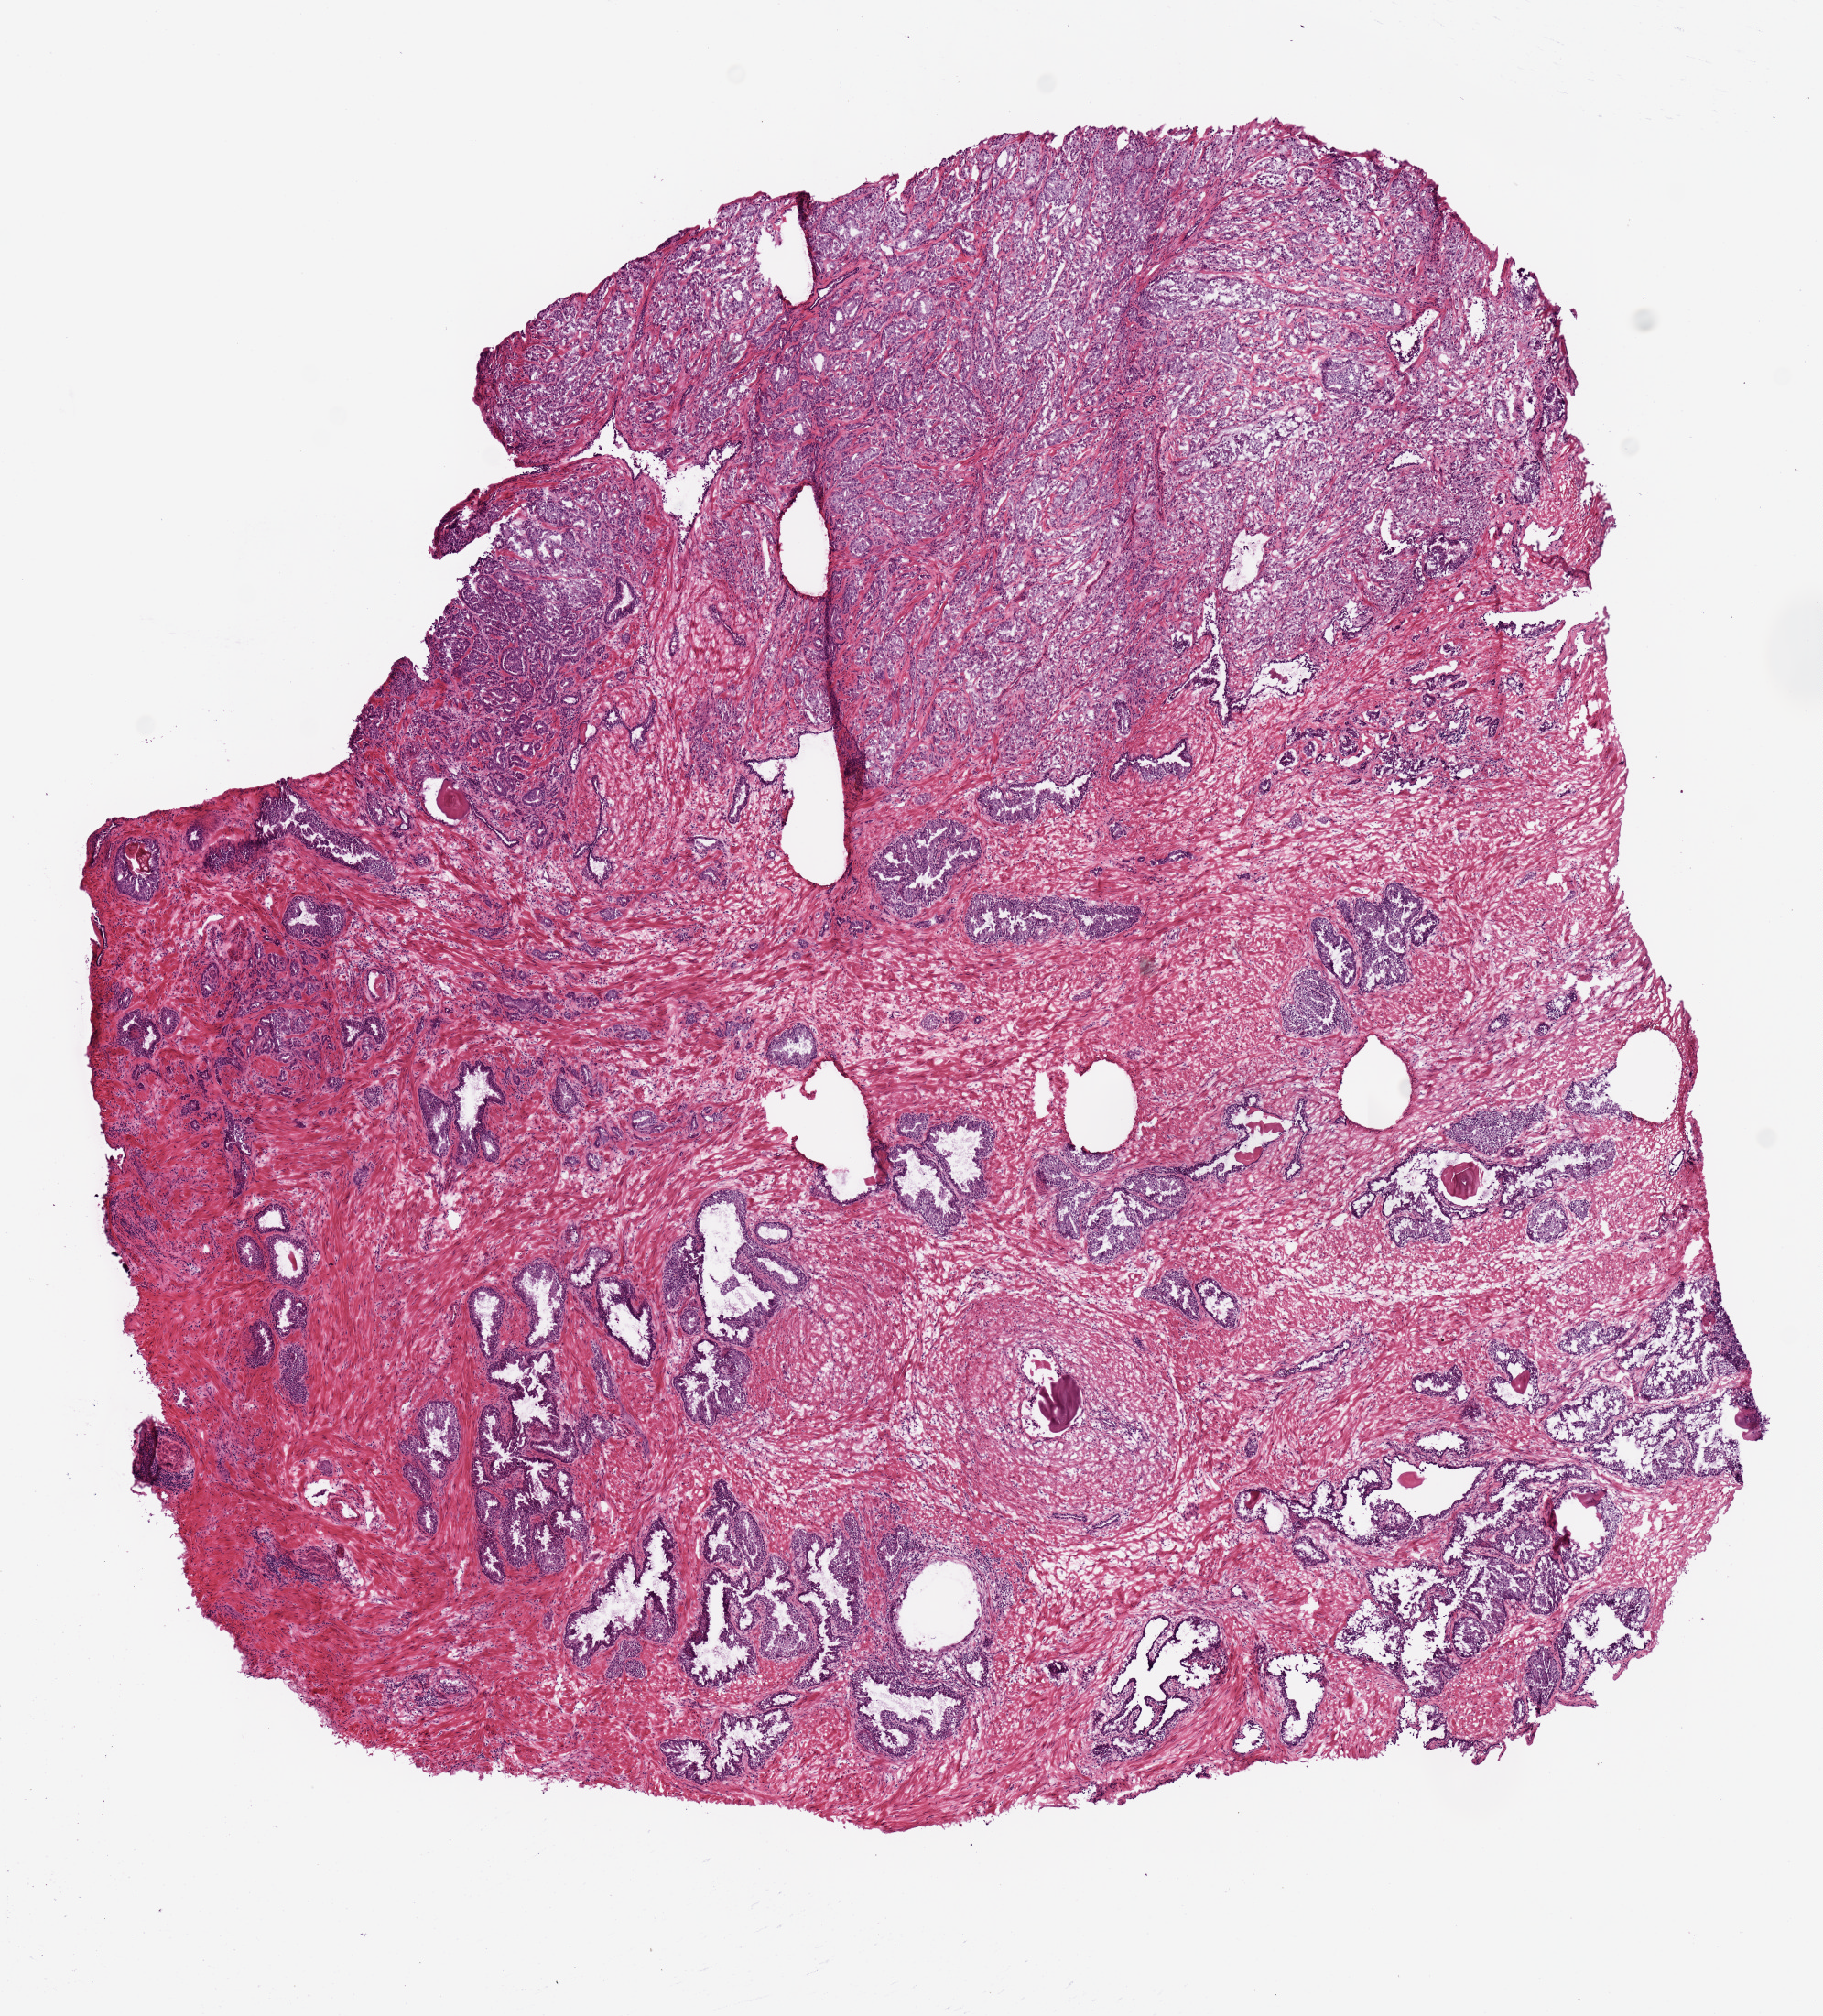
Whole-slide histology image, H&E — a low-resolution overview of the entire scanned area, about 7.9 x 8.7 mm; frozen section from the top of the tissue portion; primary tumour sample from the prostate. Male patient; age at initial diagnosis 65 years. Gleason score: 7 (4+3). Slide review estimates, as recorded: tumour cells 90%, tumour nuclei 90%, normal cells 5%, stromal cells 5%, necrosis 0%.
Pathologic diagnosis: Acinar cell carcinoma (prostate gland).